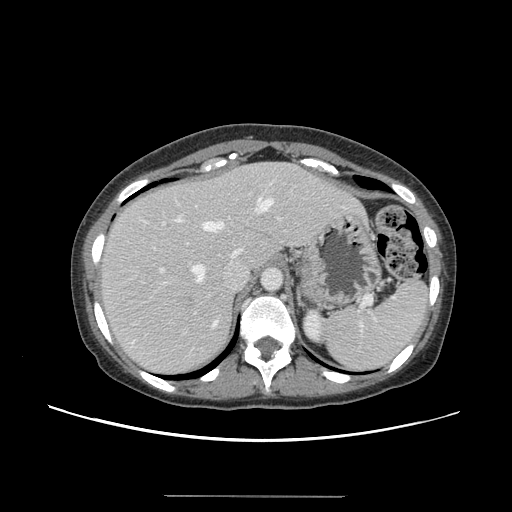
Contrast-enhanced abdominal CT, one axial slice; slice 109 of 144 in the series (ordered by position); intravenous contrast given; soft-tissue window (W 400 / L 40 HU); 512 × 512 image matrix. Female patient, age 53 years. Case-level facts recorded for this patient, not image findings: diagnosis: colorectal cancer liver metastases, imaged before liver resection; multiple liver metastases: yes; largest metastasis: 1.1 cm; disease in both lobes: no.
Structures marked on this image (outlined manually by an expert reader):
- hepatic veins: bounding box [x1, y1, x2, y2] px = [177, 198, 273, 281]
- liver: [101, 162, 362, 374]
- planned liver remnant (the part of the liver to remain after resection): [96, 162, 296, 301]
- portal vein (with intrahepatic branches): [160, 218, 281, 273]
- liver metastasis: [184, 297, 193, 303]